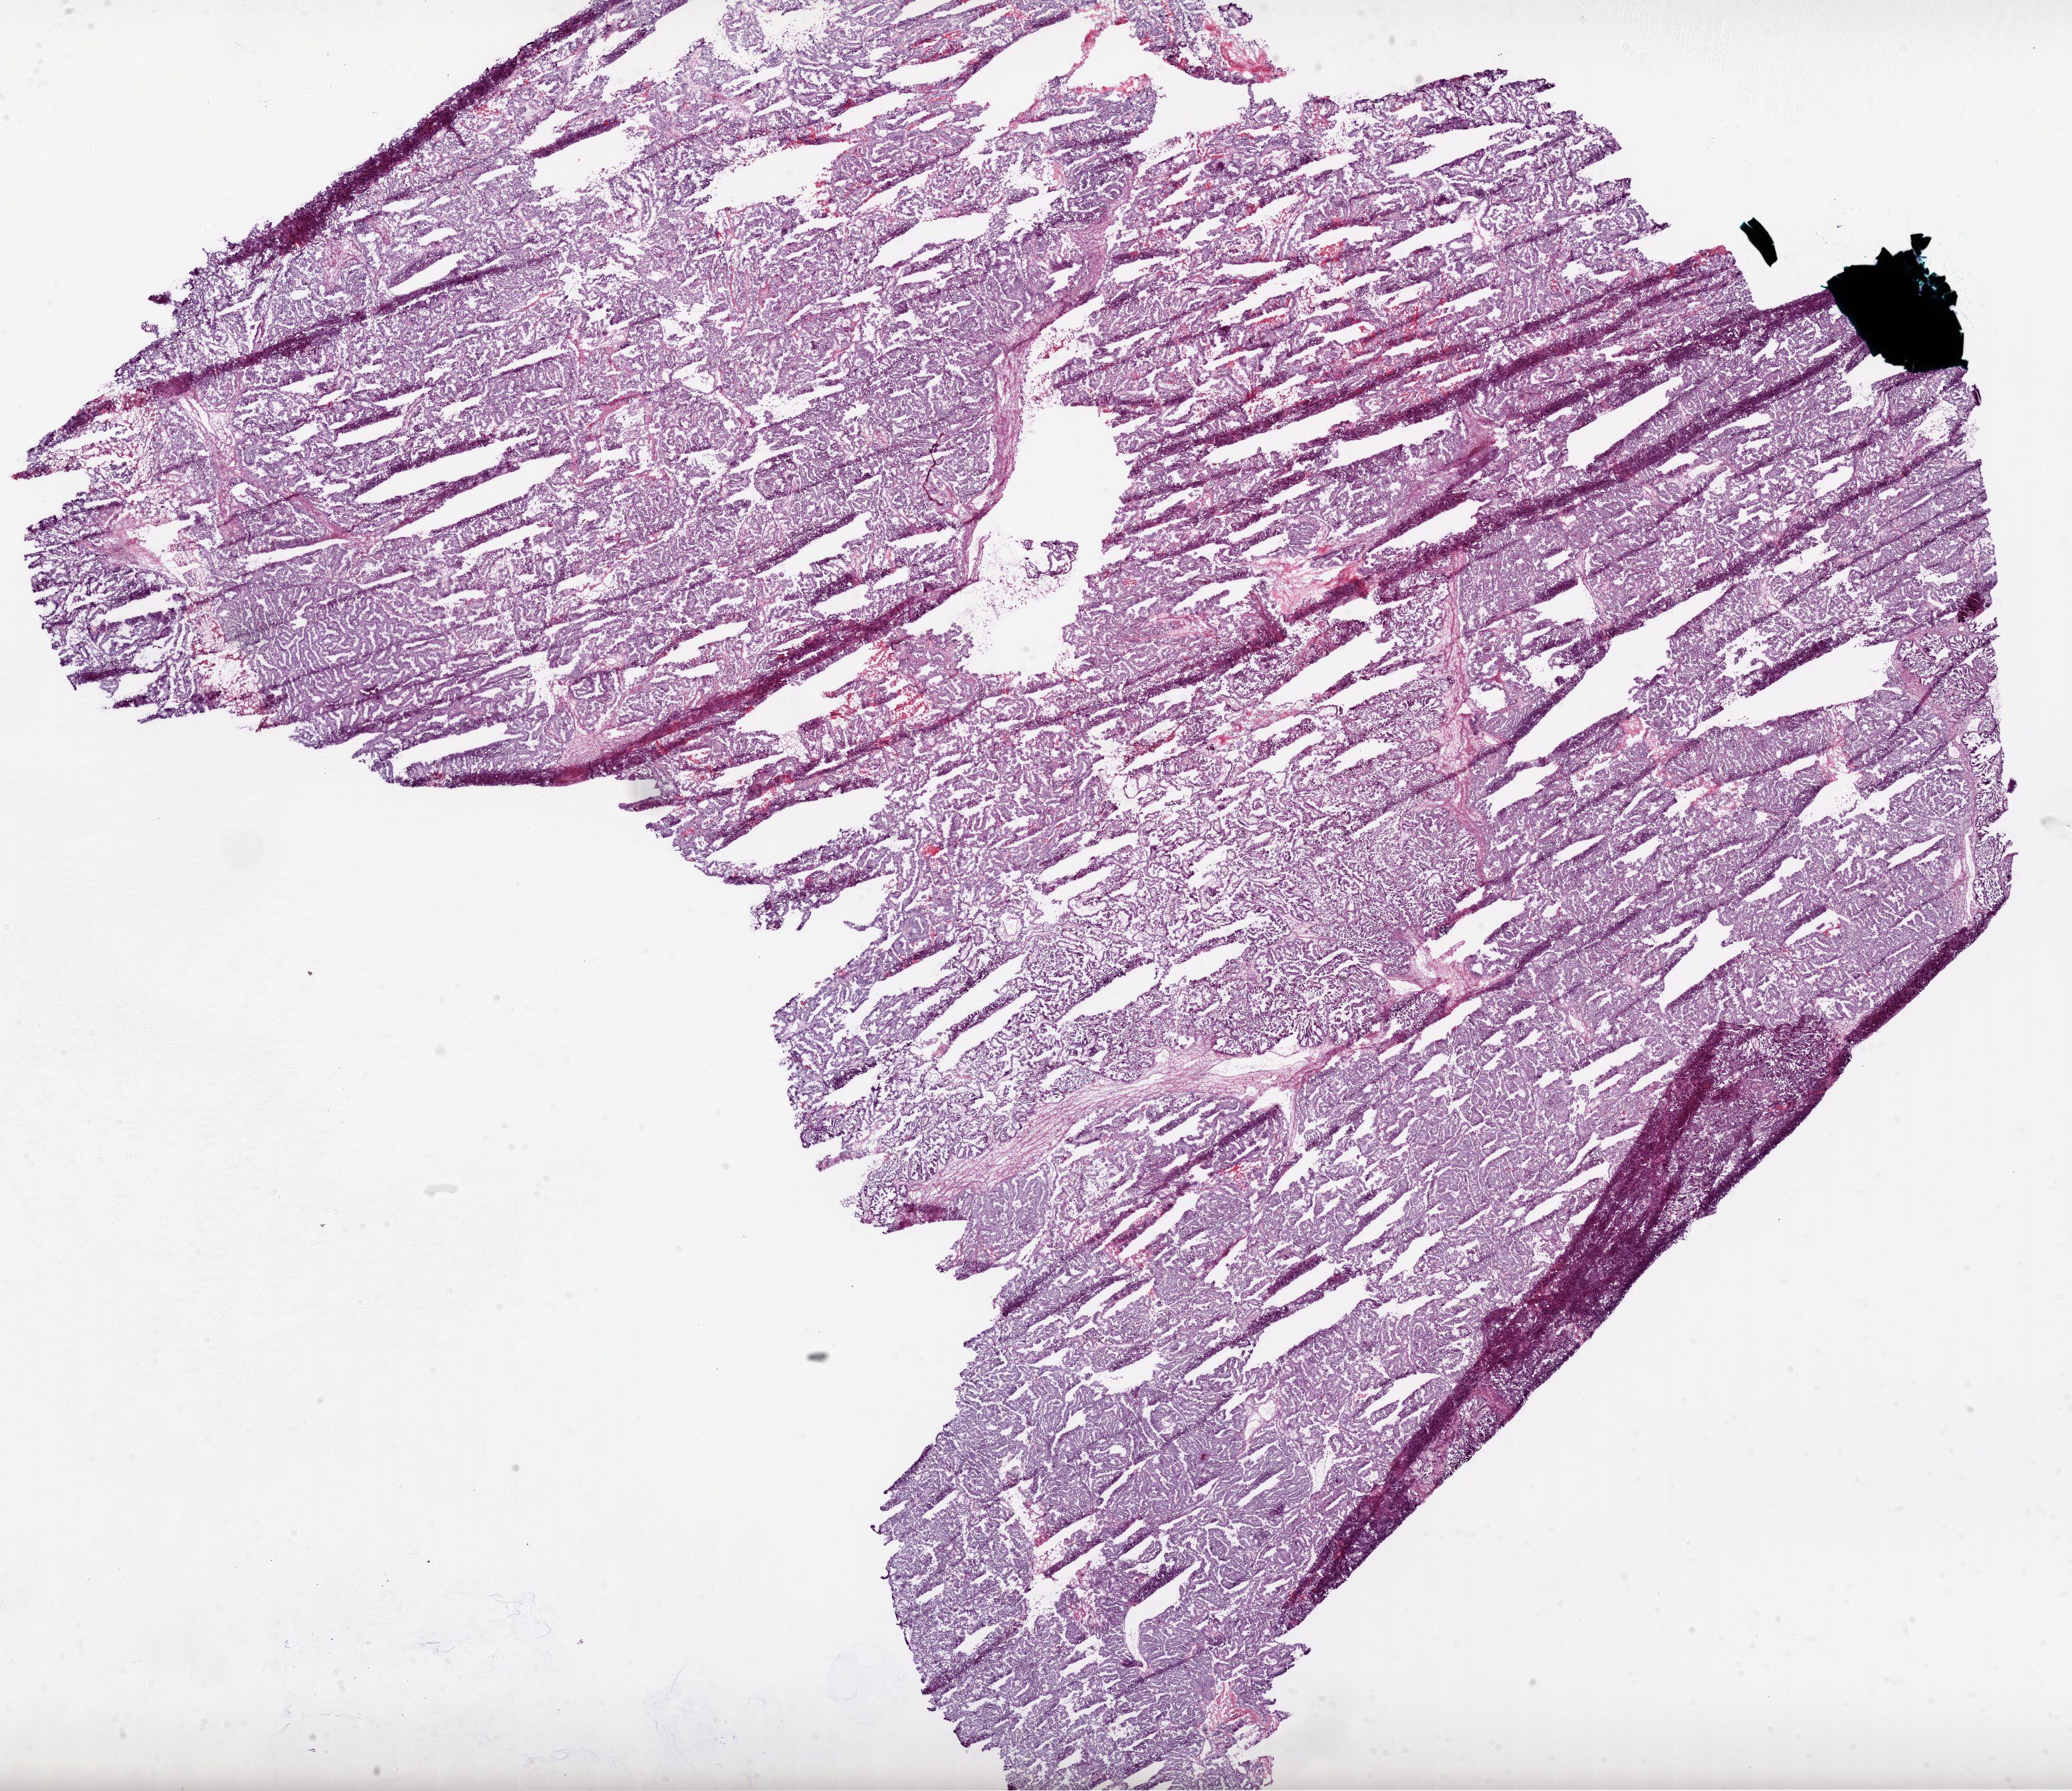
H&E whole-slide image — low-resolution overview of the scanned area, about 25.1 x 21.7 mm; frozen section; ovary, primary tumour sample. Patient: female, age at initial diagnosis 50 years. Histologic grade: G3 (poorly differentiated). Pathologist review of this section (percent, as recorded): tumour cells 95%, tumour nuclei 95%, normal cells 0%, stromal cells 5%, necrosis 0%.
FIGO stage: IIIC. Pathologic diagnosis: Serous cystadenocarcinoma, NOS.